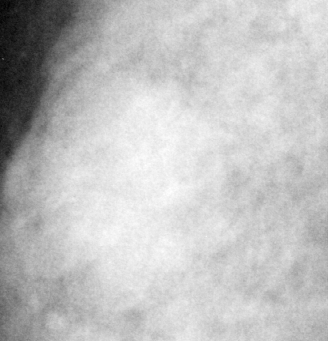
Region of interest cut from a scanned film mammogram (one marked finding), right breast, MLO view.
- Marked abnormality: mass, shape lobulated, margins microlobulated; BI-RADS assessment category 4; pathology (as recorded): benign.